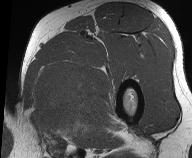
MRI of an extremity soft-tissue mass, one axial slice. Slice 41 of 61 in the series (ordered by position). MR volume resampled by the dataset authors to the PET/CT grid (not the native acquisition matrix). 192 × 158 image matrix, field of view 187 × 154 mm. Male patient. Case-level facts recorded for this patient, not image findings: histological type: pleiomorphic liposarcoma; grade: high; site of the primary tumour: left thigh.
Structures marked on this image (expert contour drawn on MRI and transferred to this co-registered scan by the dataset authors):
- gross tumour volume including surrounding oedema: bounding box [x1, y1, x2, y2] px = [32, 66, 97, 134]
- gross tumour volume (mass): [34, 71, 87, 118]